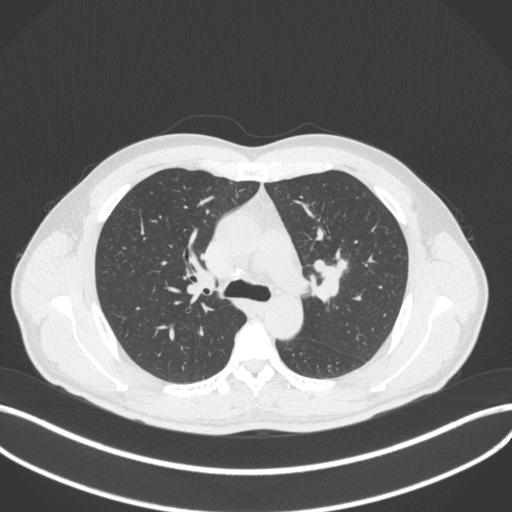
Chest CT, one axial slice; slice 279 of 383 in the series (ordered by position); lung window (W 1500 / L -600 HU); 1 mm slice thickness; 512 × 512 image matrix, field of view 400 × 400 mm. Male patient, age 50 years. Case-level facts recorded for this patient, not image findings: clinical TNM (as recorded): T1c N1 M1b.
Annotated regions visible in this slice (bounding box drawn by a radiologist):
- lung tumour (recorded histology: squamous cell carcinoma): bounding box [x1, y1, x2, y2] px = [307, 256, 348, 305]